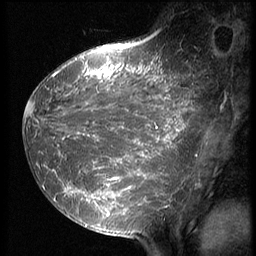
Breast MRI (dynamic contrast-enhanced), one sagittal slice; 3 images stored at this slice position (order not interpretable as contrast timing); 1.5 T; TE 4.2 ms, TR 9 ms; 2.5 mm slice thickness; 256 × 256 image matrix, field of view 180 × 180 mm. Female patient, age 39 years. Case-level facts recorded for this patient, not image findings: setting: breast cancer imaged before/during neoadjuvant chemotherapy; receptor status: HER2-positive.
Structures marked on this image (semi-automatic segmentation, software-assisted and operator-edited):
- analysis volume of interest (the breast-tissue region the enhancement analysis was run in; not a lesion): box from (x=23, y=47) to (x=208, y=239) px
- tumour enhancement mask (voxels above the 140 % enhancement threshold inside the analysis volume of interest): (x=24, y=47)–(x=201, y=218)